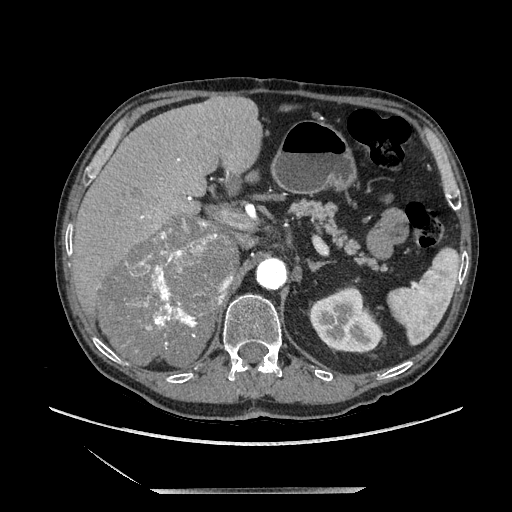
Contrast-enhanced abdominal CT, one axial slice; soft-tissue window (W 400 / L 40 HU); 1.25 mm slice thickness; 512 × 512 image matrix, field of view 420 × 420 mm. Male patient. Case-level facts recorded for this patient, not image findings: diagnosis: adrenocortical carcinoma; tumour side: right adrenal; tumour size at pathology: 16 cm; Ki-67 index: 17 %; stage (as recorded): 3.
Annotated regions visible in this slice (semi-automatically segmented with operator editing):
- mass: box from (x=102, y=219) to (x=237, y=367) px